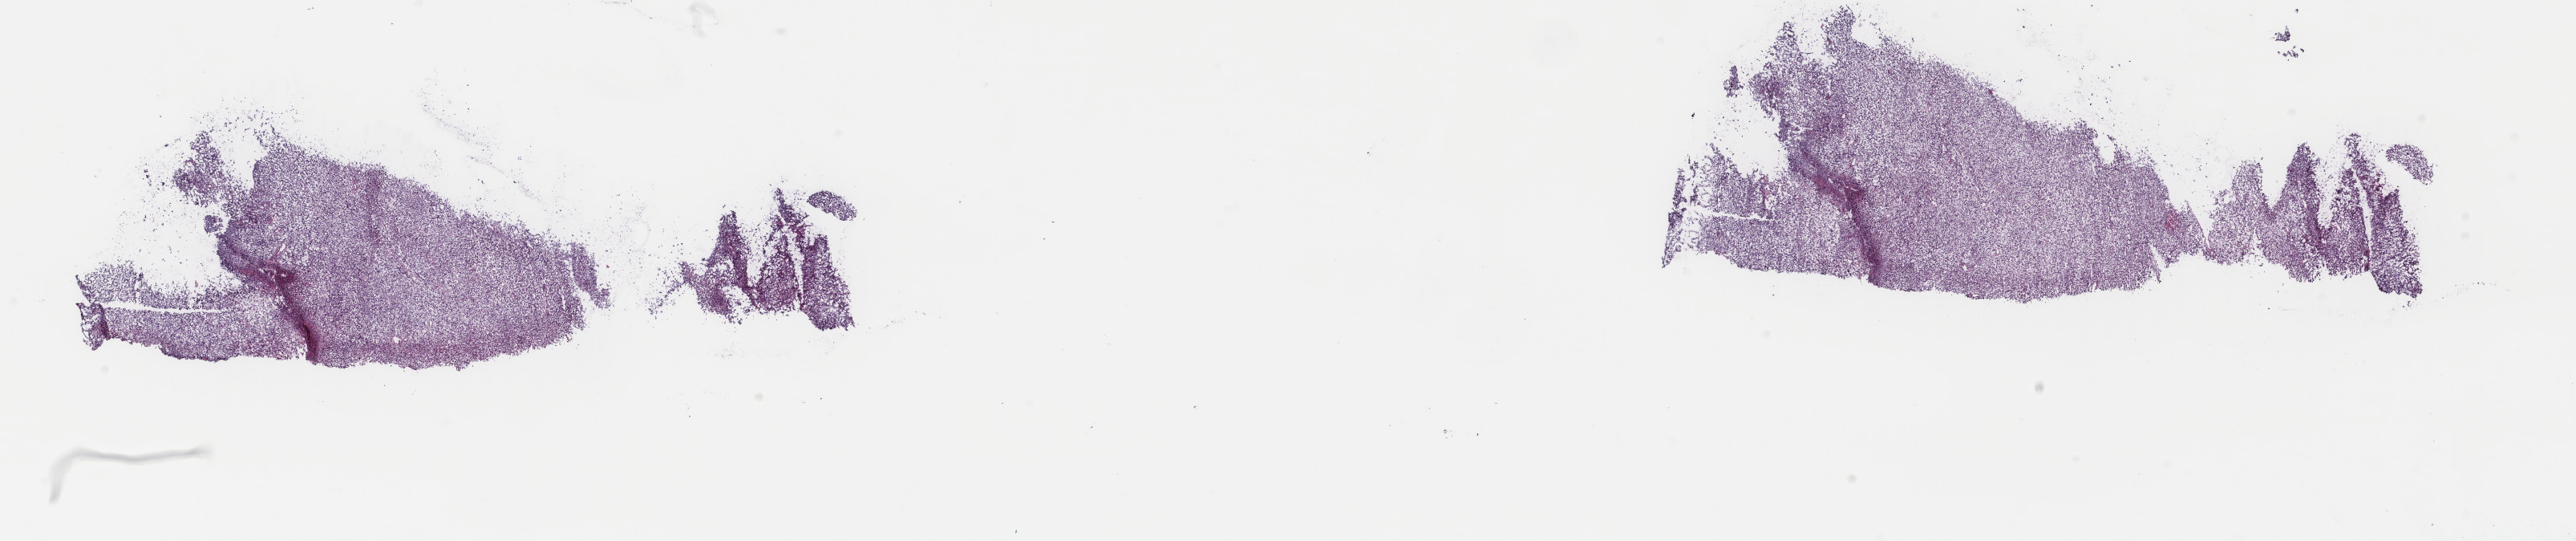
H&E-stained whole-slide image — low-resolution overview of the scanned area, about 25.5 x 5.4 mm, frozen section, primary tumour sample from the uterus. Patient: female, age at initial diagnosis 76 years. Composition of this section per pathologist review: tumour cells 90%, tumour nuclei 90%, normal cells 0%, stromal cells 5%, necrosis 5%. Infiltration values recorded for this section: lymphocyte infiltration 5%, monocyte infiltration 0%, neutrophil infiltration 0%.
Histologic diagnosis: Leiomyosarcoma, NOS.